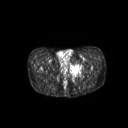
FDG PET of an extremity soft-tissue mass (from a PET/CT study), one axial slice; position 42 of 267 along the scan axis; 3.27 mm slice thickness; 128 × 128 image matrix. Male patient, age 59 years. From the clinical record (not read from this slice): histological type: pleiomorphic liposarcoma; grade: high; site of the primary tumour: left thigh.
Annotated regions visible in this slice (expert contour drawn on MRI and transferred to this co-registered scan by the dataset authors):
- gross tumour volume including surrounding oedema: bounding box <70,64,84,78> (left, top, right, bottom; pixels)
- gross tumour volume (mass): <71,64,82,73>